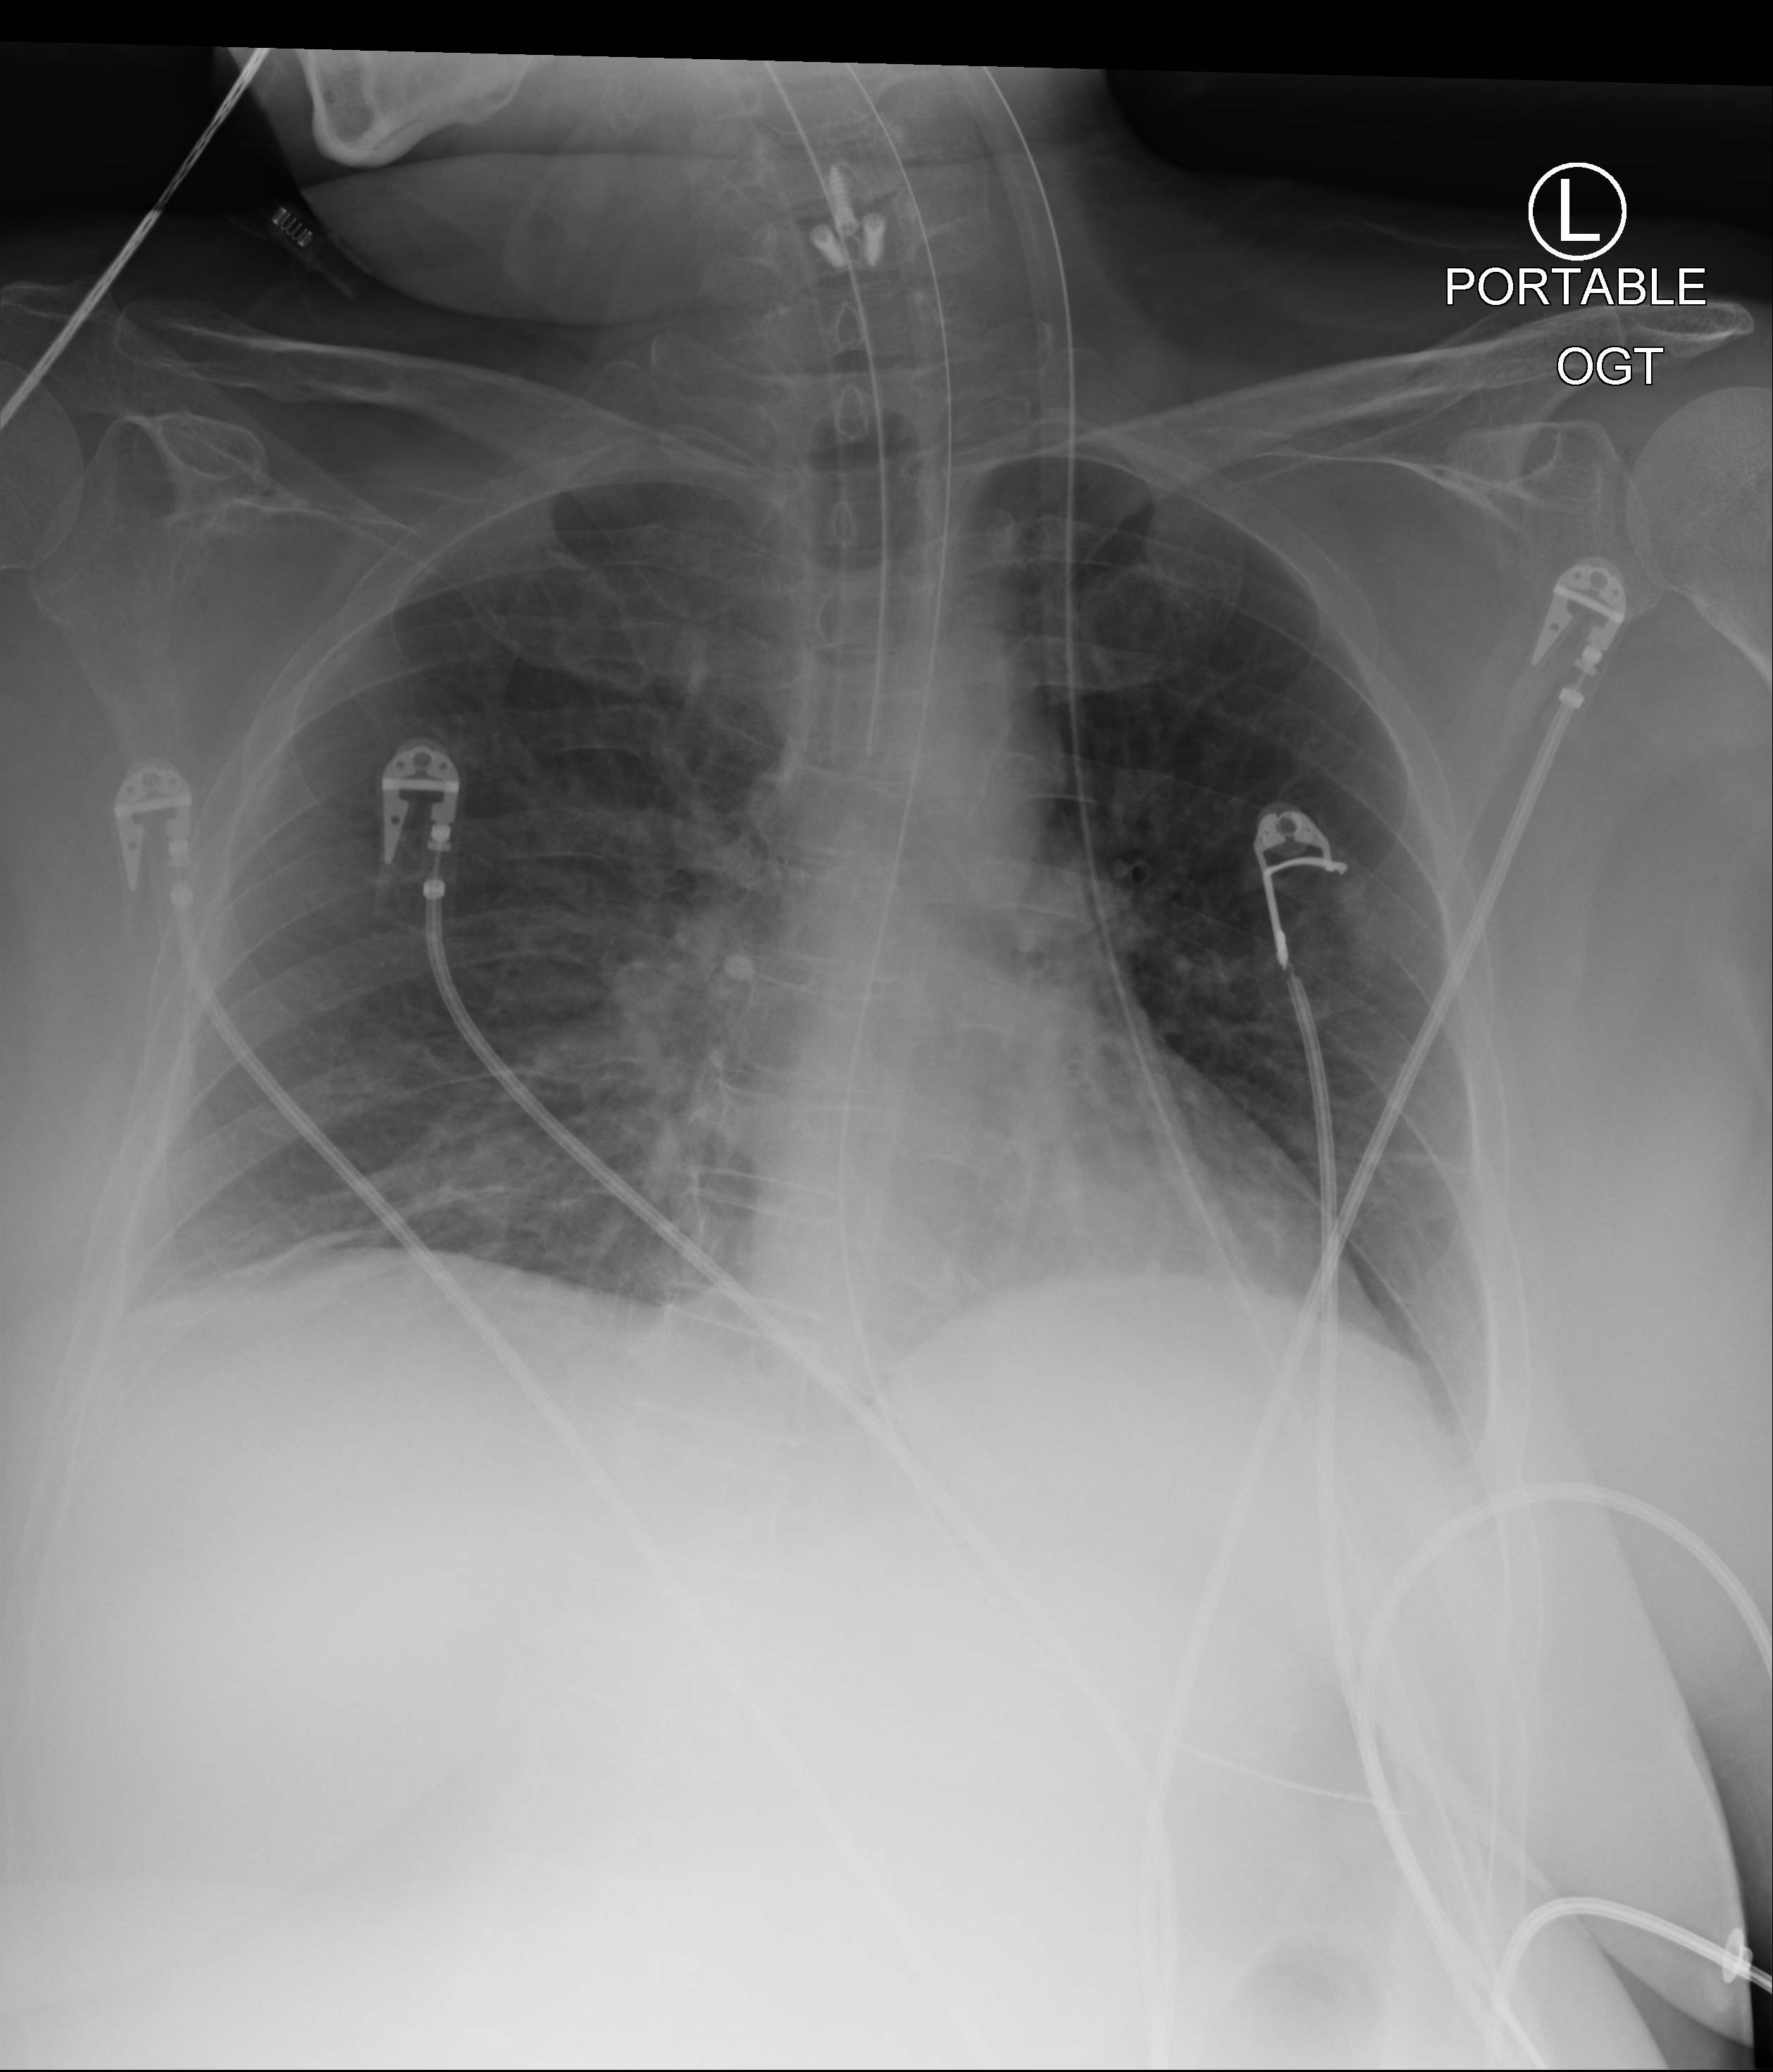
Portable chest radiograph. Female patient hospitalised with COVID-19, age 18–59 years.
From the hospital-stay record, not from the radiograph (when in the stay this image was taken is not recorded): admitted to intensive care during this hospital stay: yes.